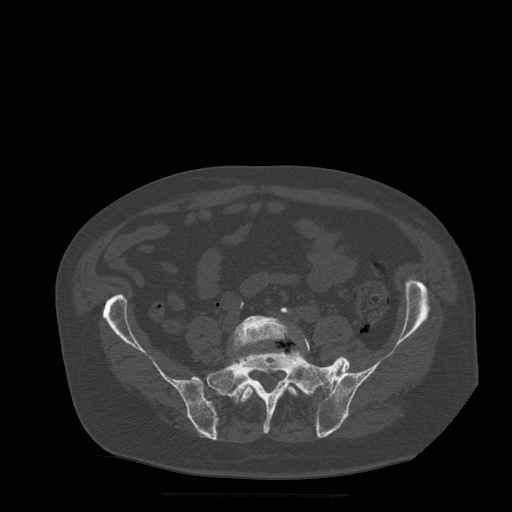
CT including the spine, one axial slice. Position 73 of 522 along the scan axis. Bone window (W 1800 / L 400 HU). 1.25 mm slice thickness. 512 × 512 image matrix. Patient age 72 years. From the clinical record (not read from this slice): primary cancer: prostate.
Structures marked on this image (semi-automatic segmentation, software-assisted and operator-edited):
- L5 vertebra: bounding box <231,316,310,402> (left, top, right, bottom; pixels)